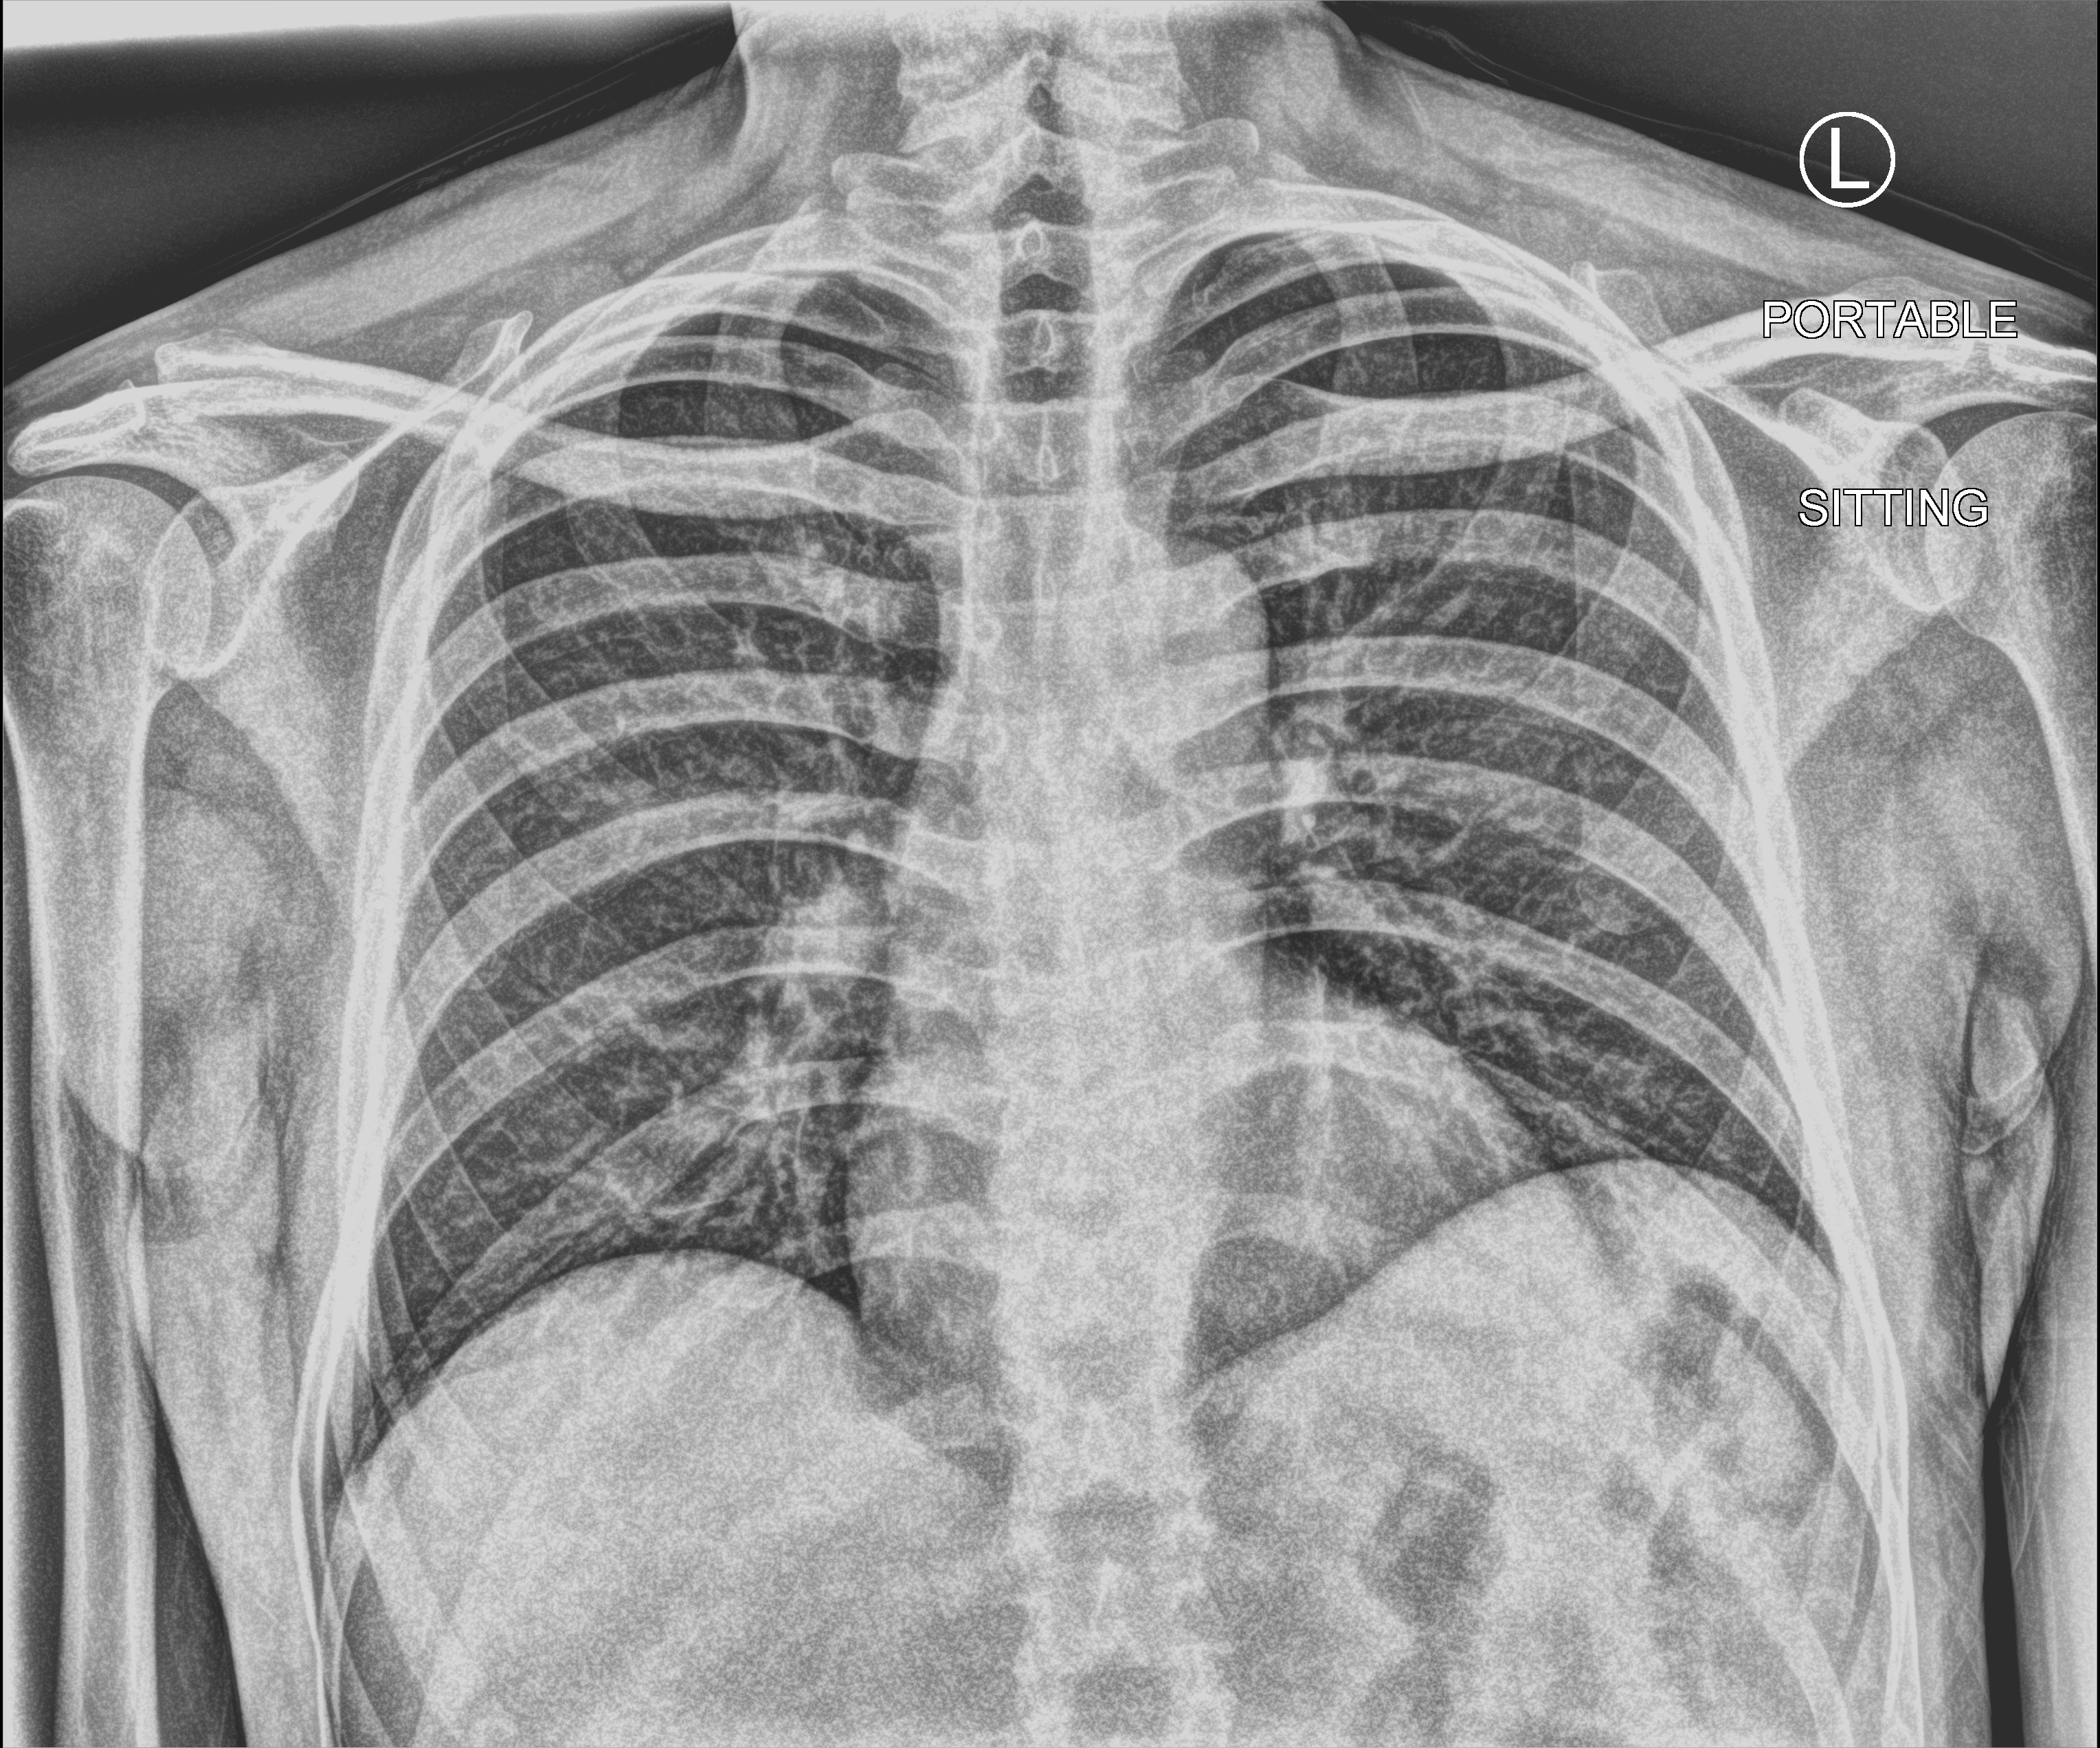
Portable chest radiograph, anteroposterior (AP) projection. Male patient hospitalised with COVID-19, age 18–59 years.
Admission-level facts for this patient (not findings on this image; timing relative to this image not recorded):
- length of hospital stay: 1 day